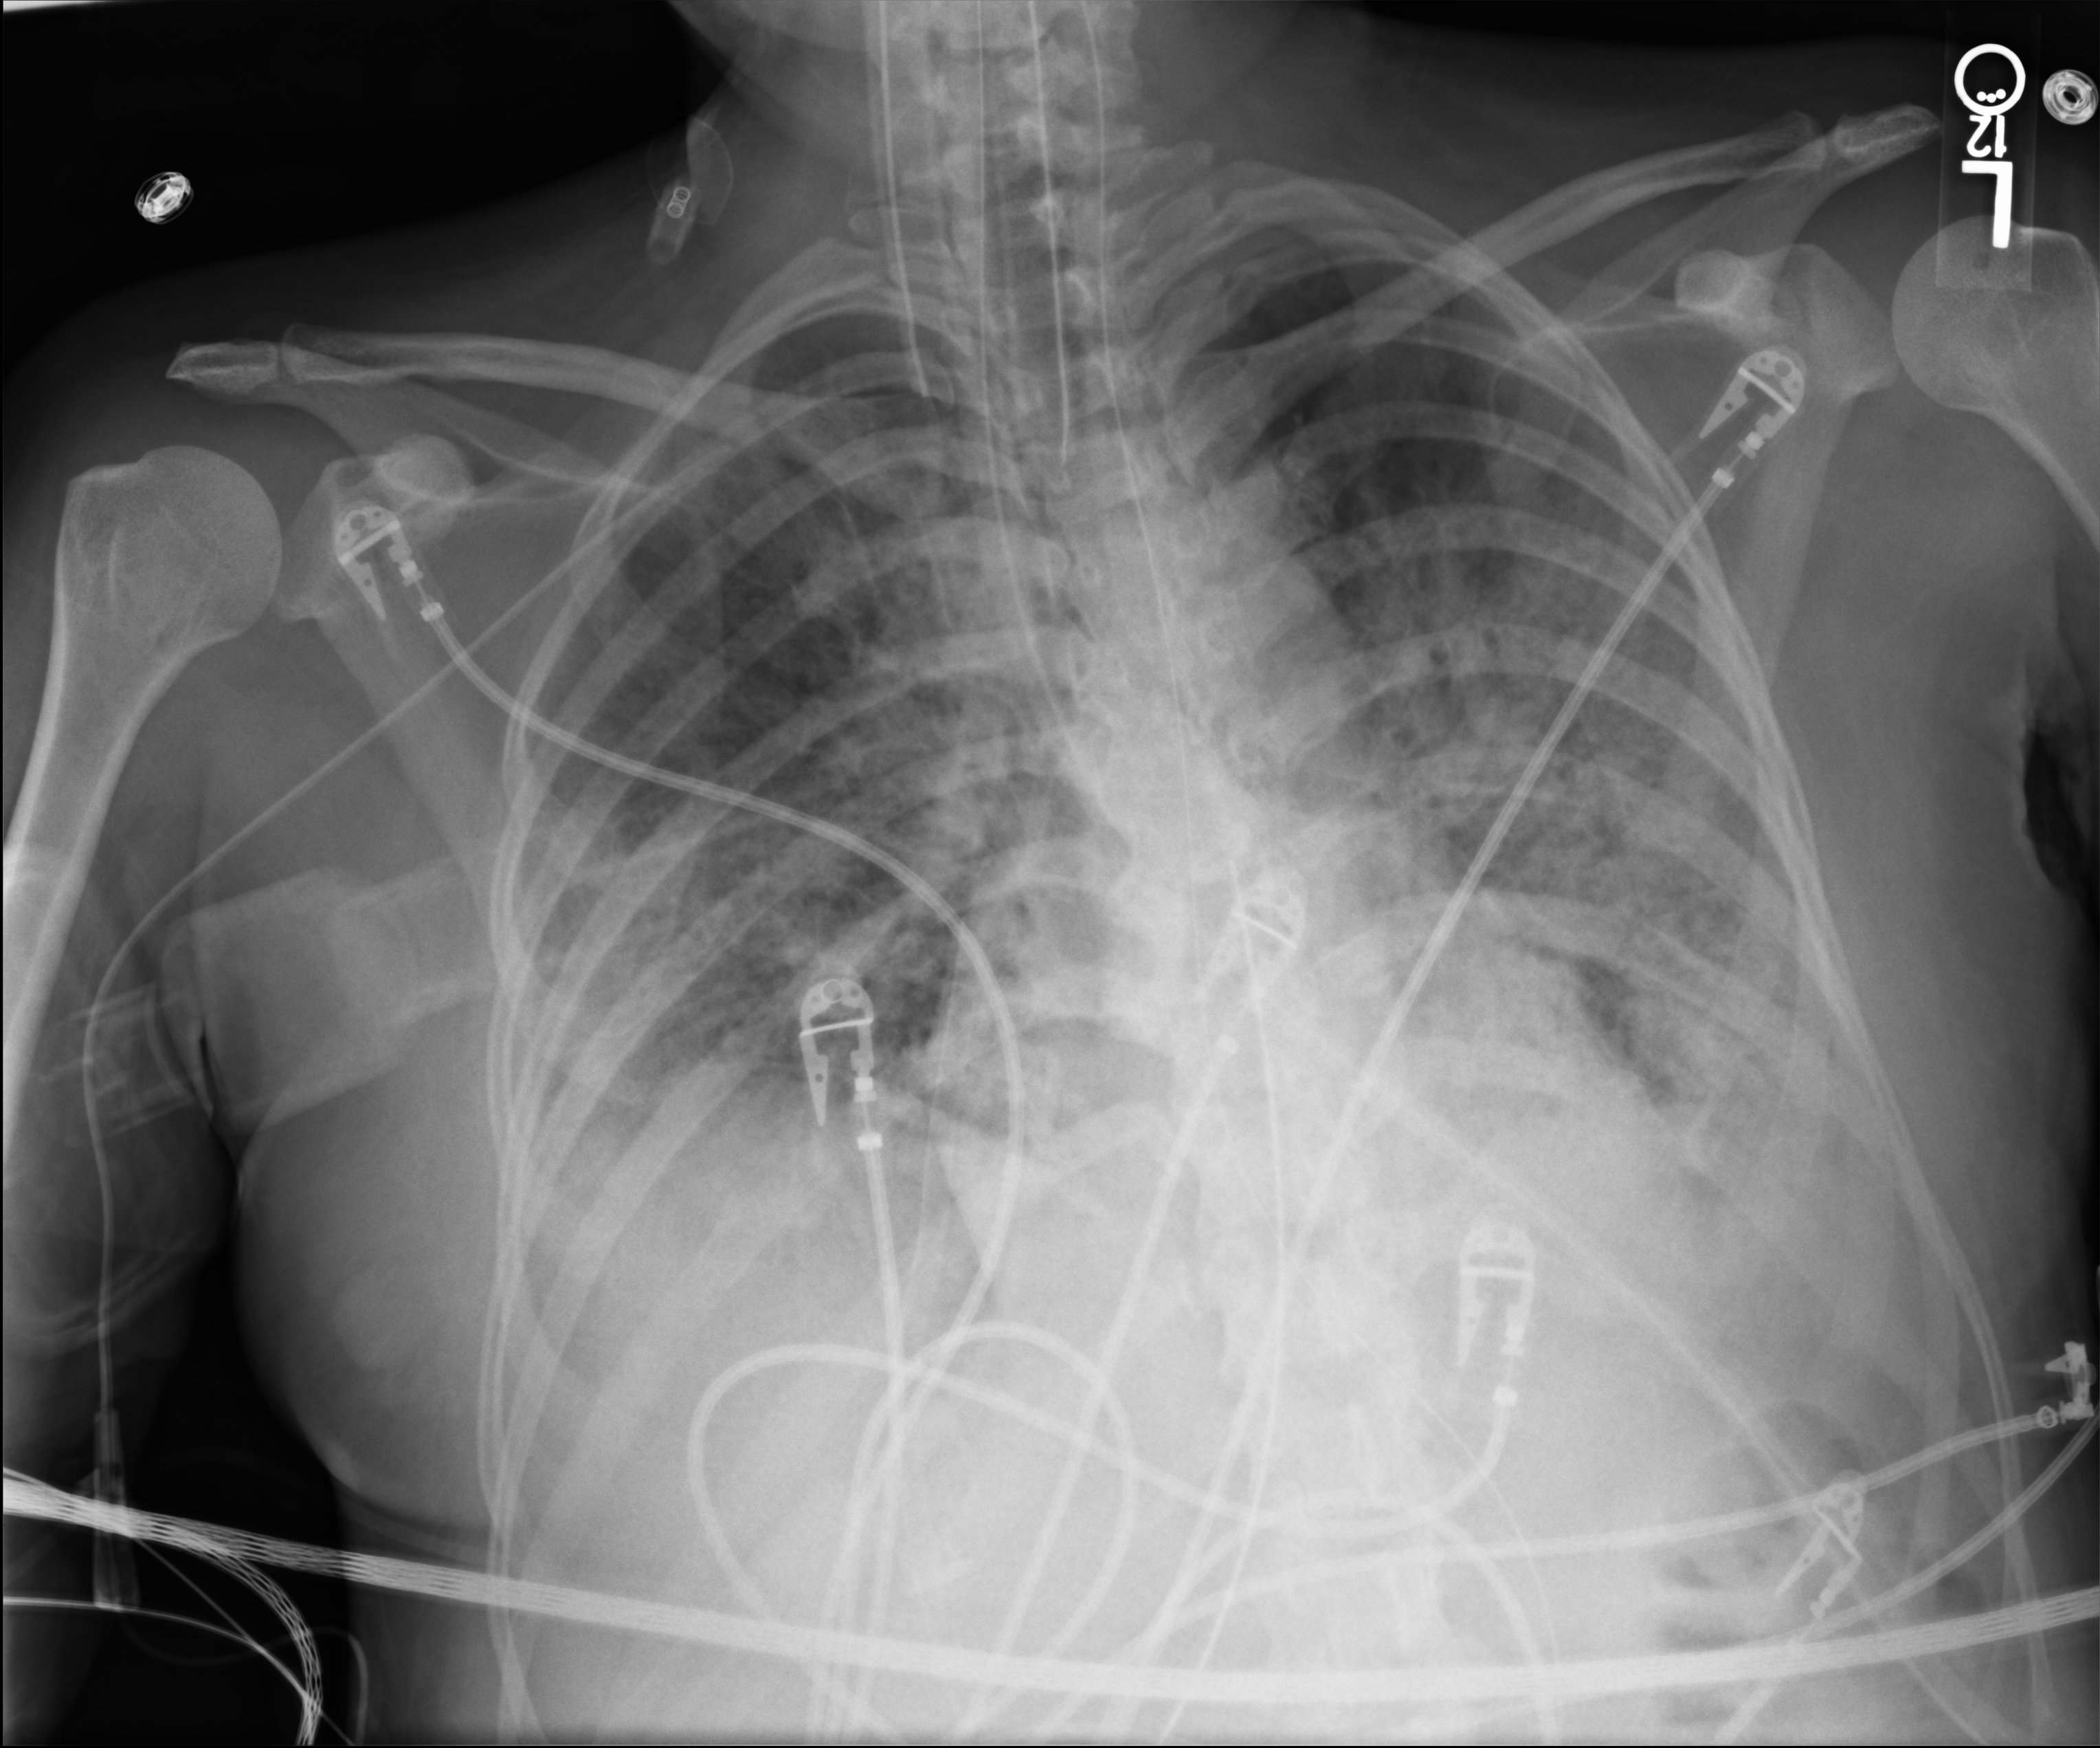
Bedside chest radiograph (computed radiography); anteroposterior (AP) projection. Female patient hospitalised with COVID-19, age 18–59 years.
Admission-level facts for this patient (not findings on this image; timing relative to this image not recorded): admitted to intensive care during this hospital stay: yes.